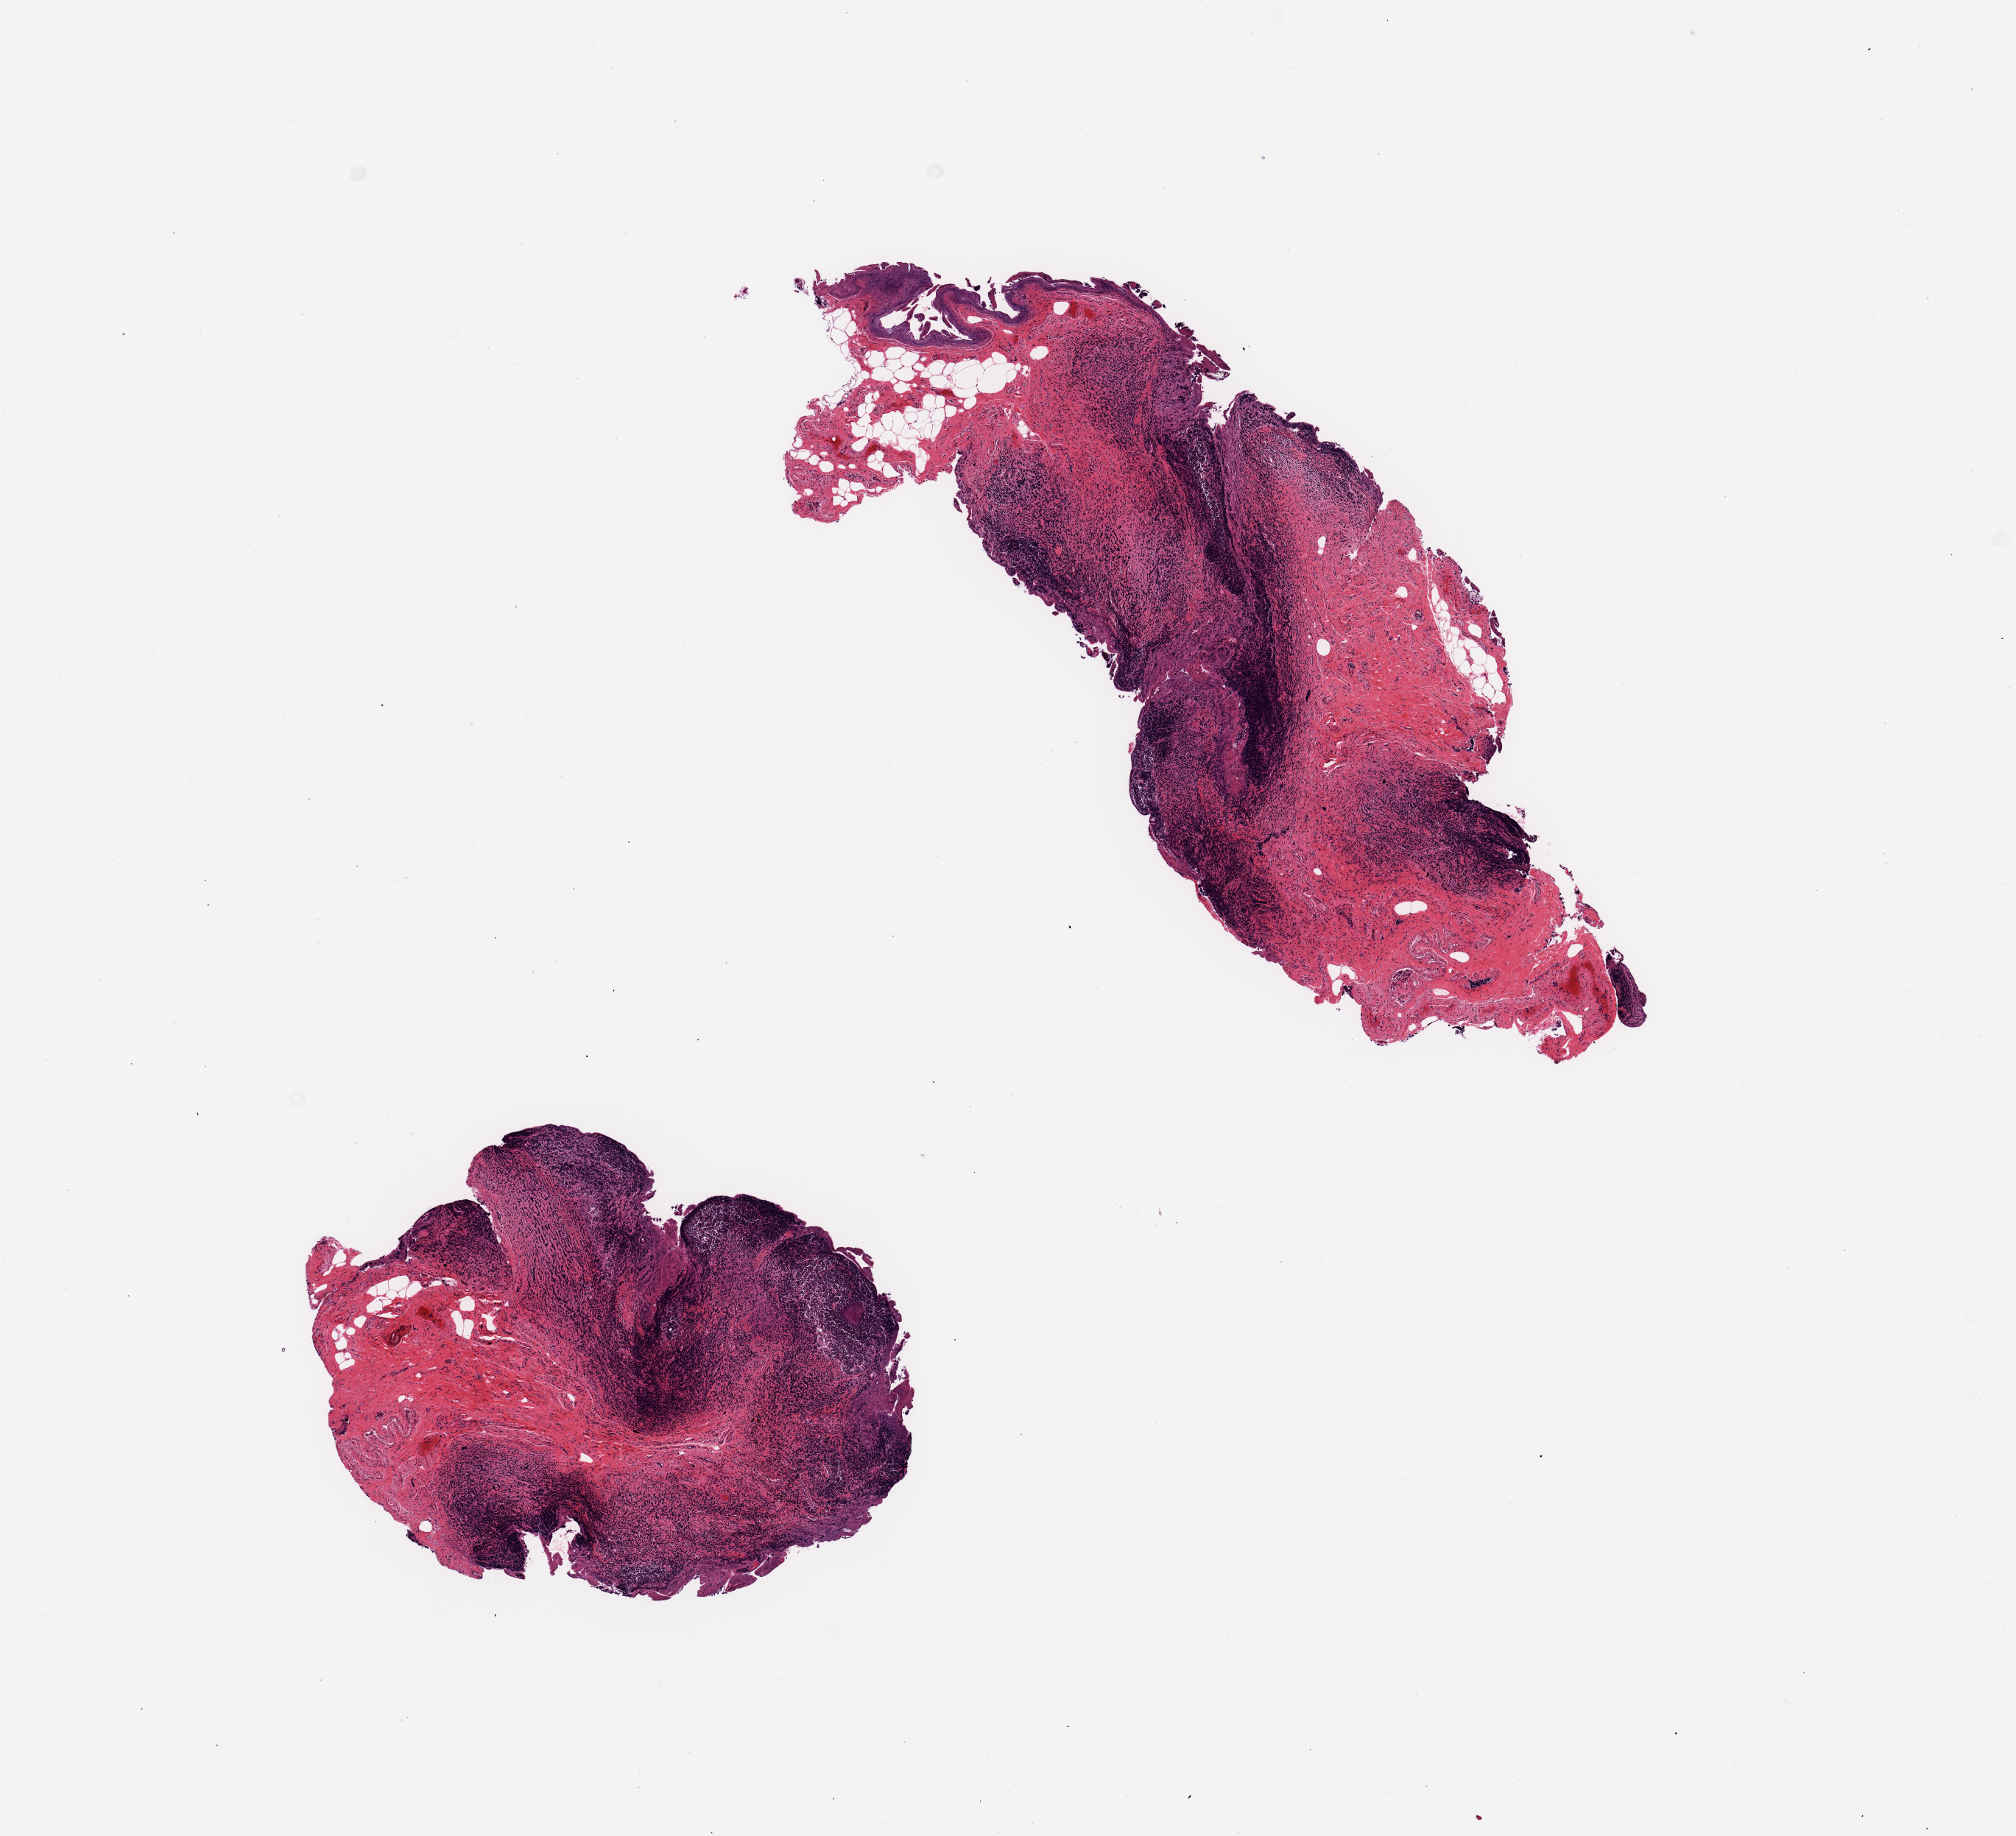
H&E whole-slide image — shown as a low-resolution overview of the whole scanned area (about 10.8 x 9.9 mm, from a 20x scan). PAXgene-fixed, paraffin-embedded tissue. Section of ileum (target tissue). Donor tissue sample. Donor sex: male.
* review note (as recorded): 2 pieces; ample lymphoid tissue, but some is autolyzed